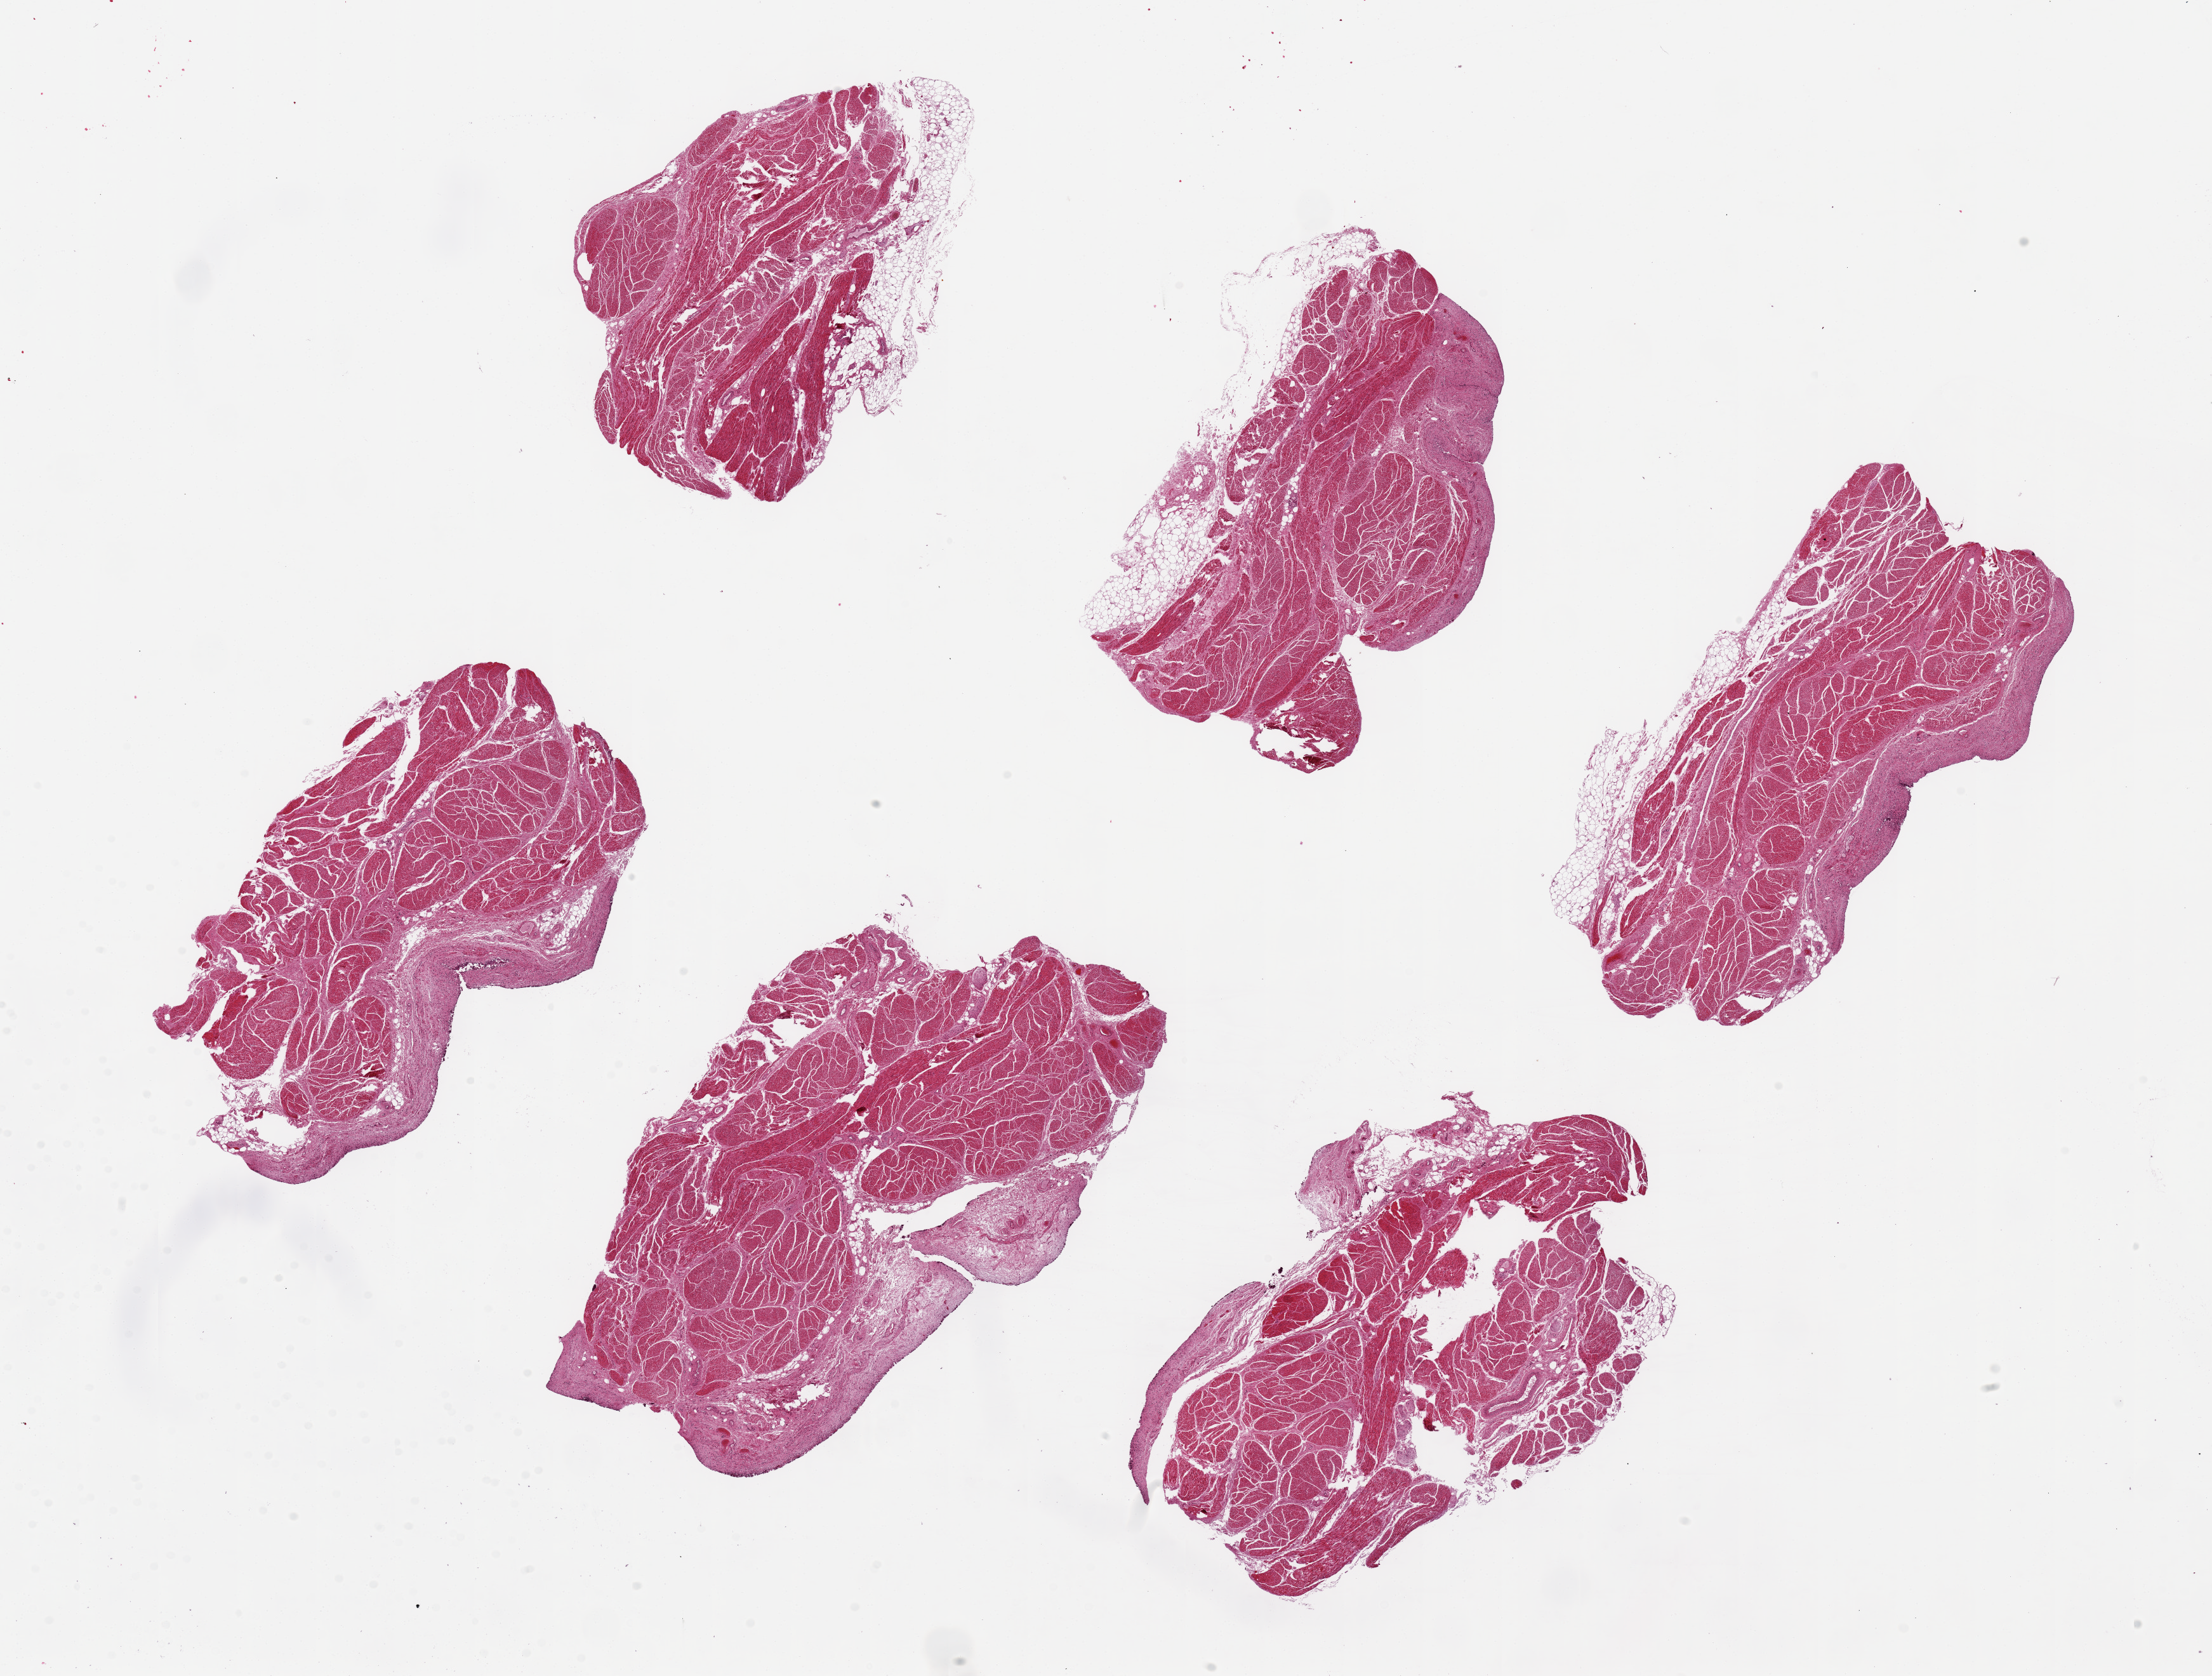
Digitized H&E-stained section, brightfield — low-resolution overview of the scanned area, about 27.6 x 20.9 mm (acquisition: 20x scan); PAXgene-fixed, paraffin-embedded tissue; sampled site (target tissue): urinary bladder; donor tissue sample. Female donor.
- review note (as recorded): 6 pieces up to 8x4 mm; mucosa totally sloughed; muscle adequate; some perimural adipose